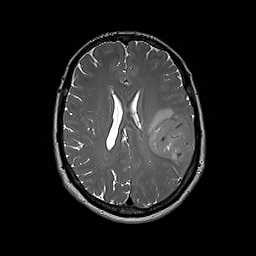
Brain MRI from a brain-tumour surgery series, one axial slice; position 85 of 192 along the scan axis; 1 mm slice thickness; 256 × 256 image matrix. From the clinical record (not read from this slice): histopathology: Glioblastoma; WHO grade: 4; IDH mutation: no; tumour location: Left Frontal.
Annotated regions visible in this slice (outlined manually by an expert reader):
- tumour: bounding box (x1, y1, x2, y2) in pixels: (149, 115, 195, 164)